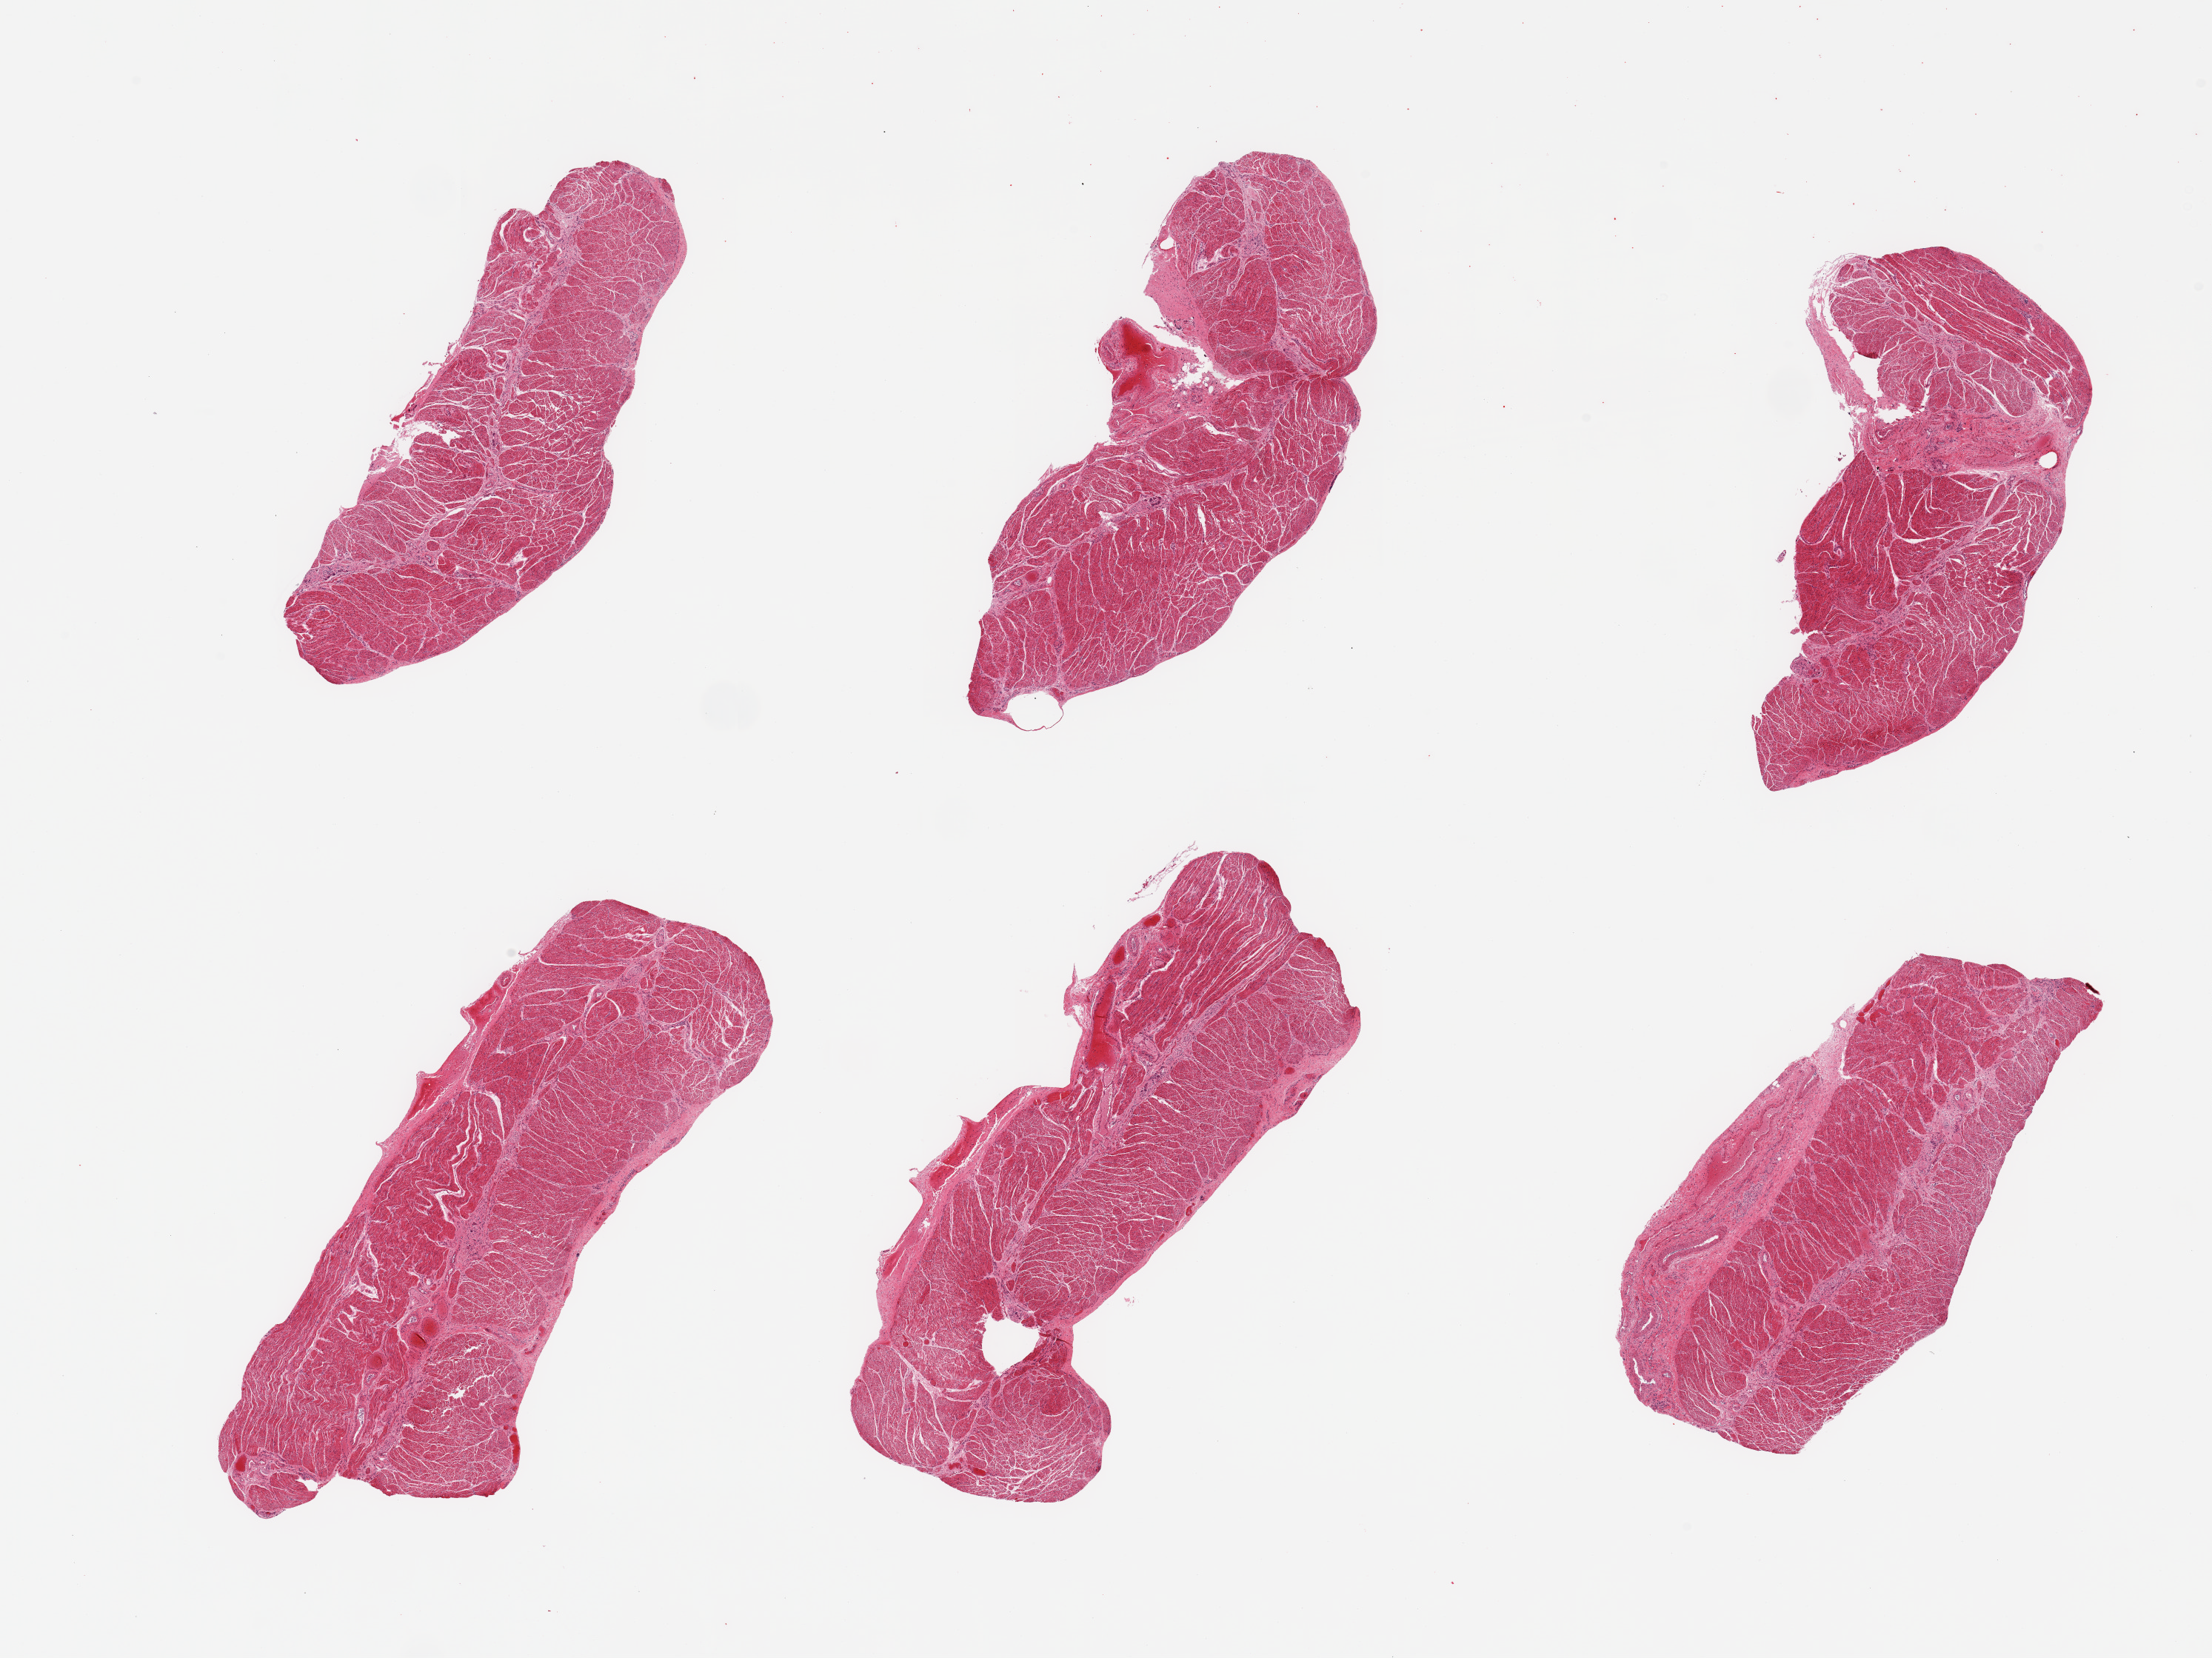
Digitized haematoxylin and eosin-stained section, a low-resolution overview of the entire scanned area, about 23.6 x 17.7 mm, PAXgene-fixed paraffin-embedded (PFPE) section, target tissue: esophageal muscle, donor tissue sample. Donor sex: female.
Pathologist's review note for this sample: 6 pieces; well trimmed muscularis.